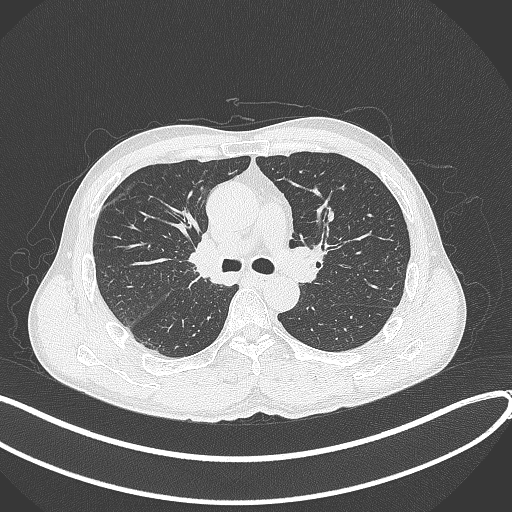
Chest CT, one axial slice. Position 240 of 409 along the scan axis. 120 kVp. Lung window (W 1500 / L -600 HU). 1 mm slice thickness. 512 × 512 image matrix, field of view 400 × 400 mm. Patient: male, 53 years. Case-level facts recorded for this patient, not image findings: clinical TNM (as recorded): T1b N0 M0.
Annotated regions visible in this slice (bounding box drawn by a radiologist):
- lung tumour (recorded histology: squamous cell carcinoma): box from (x=184, y=230) to (x=225, y=281) px